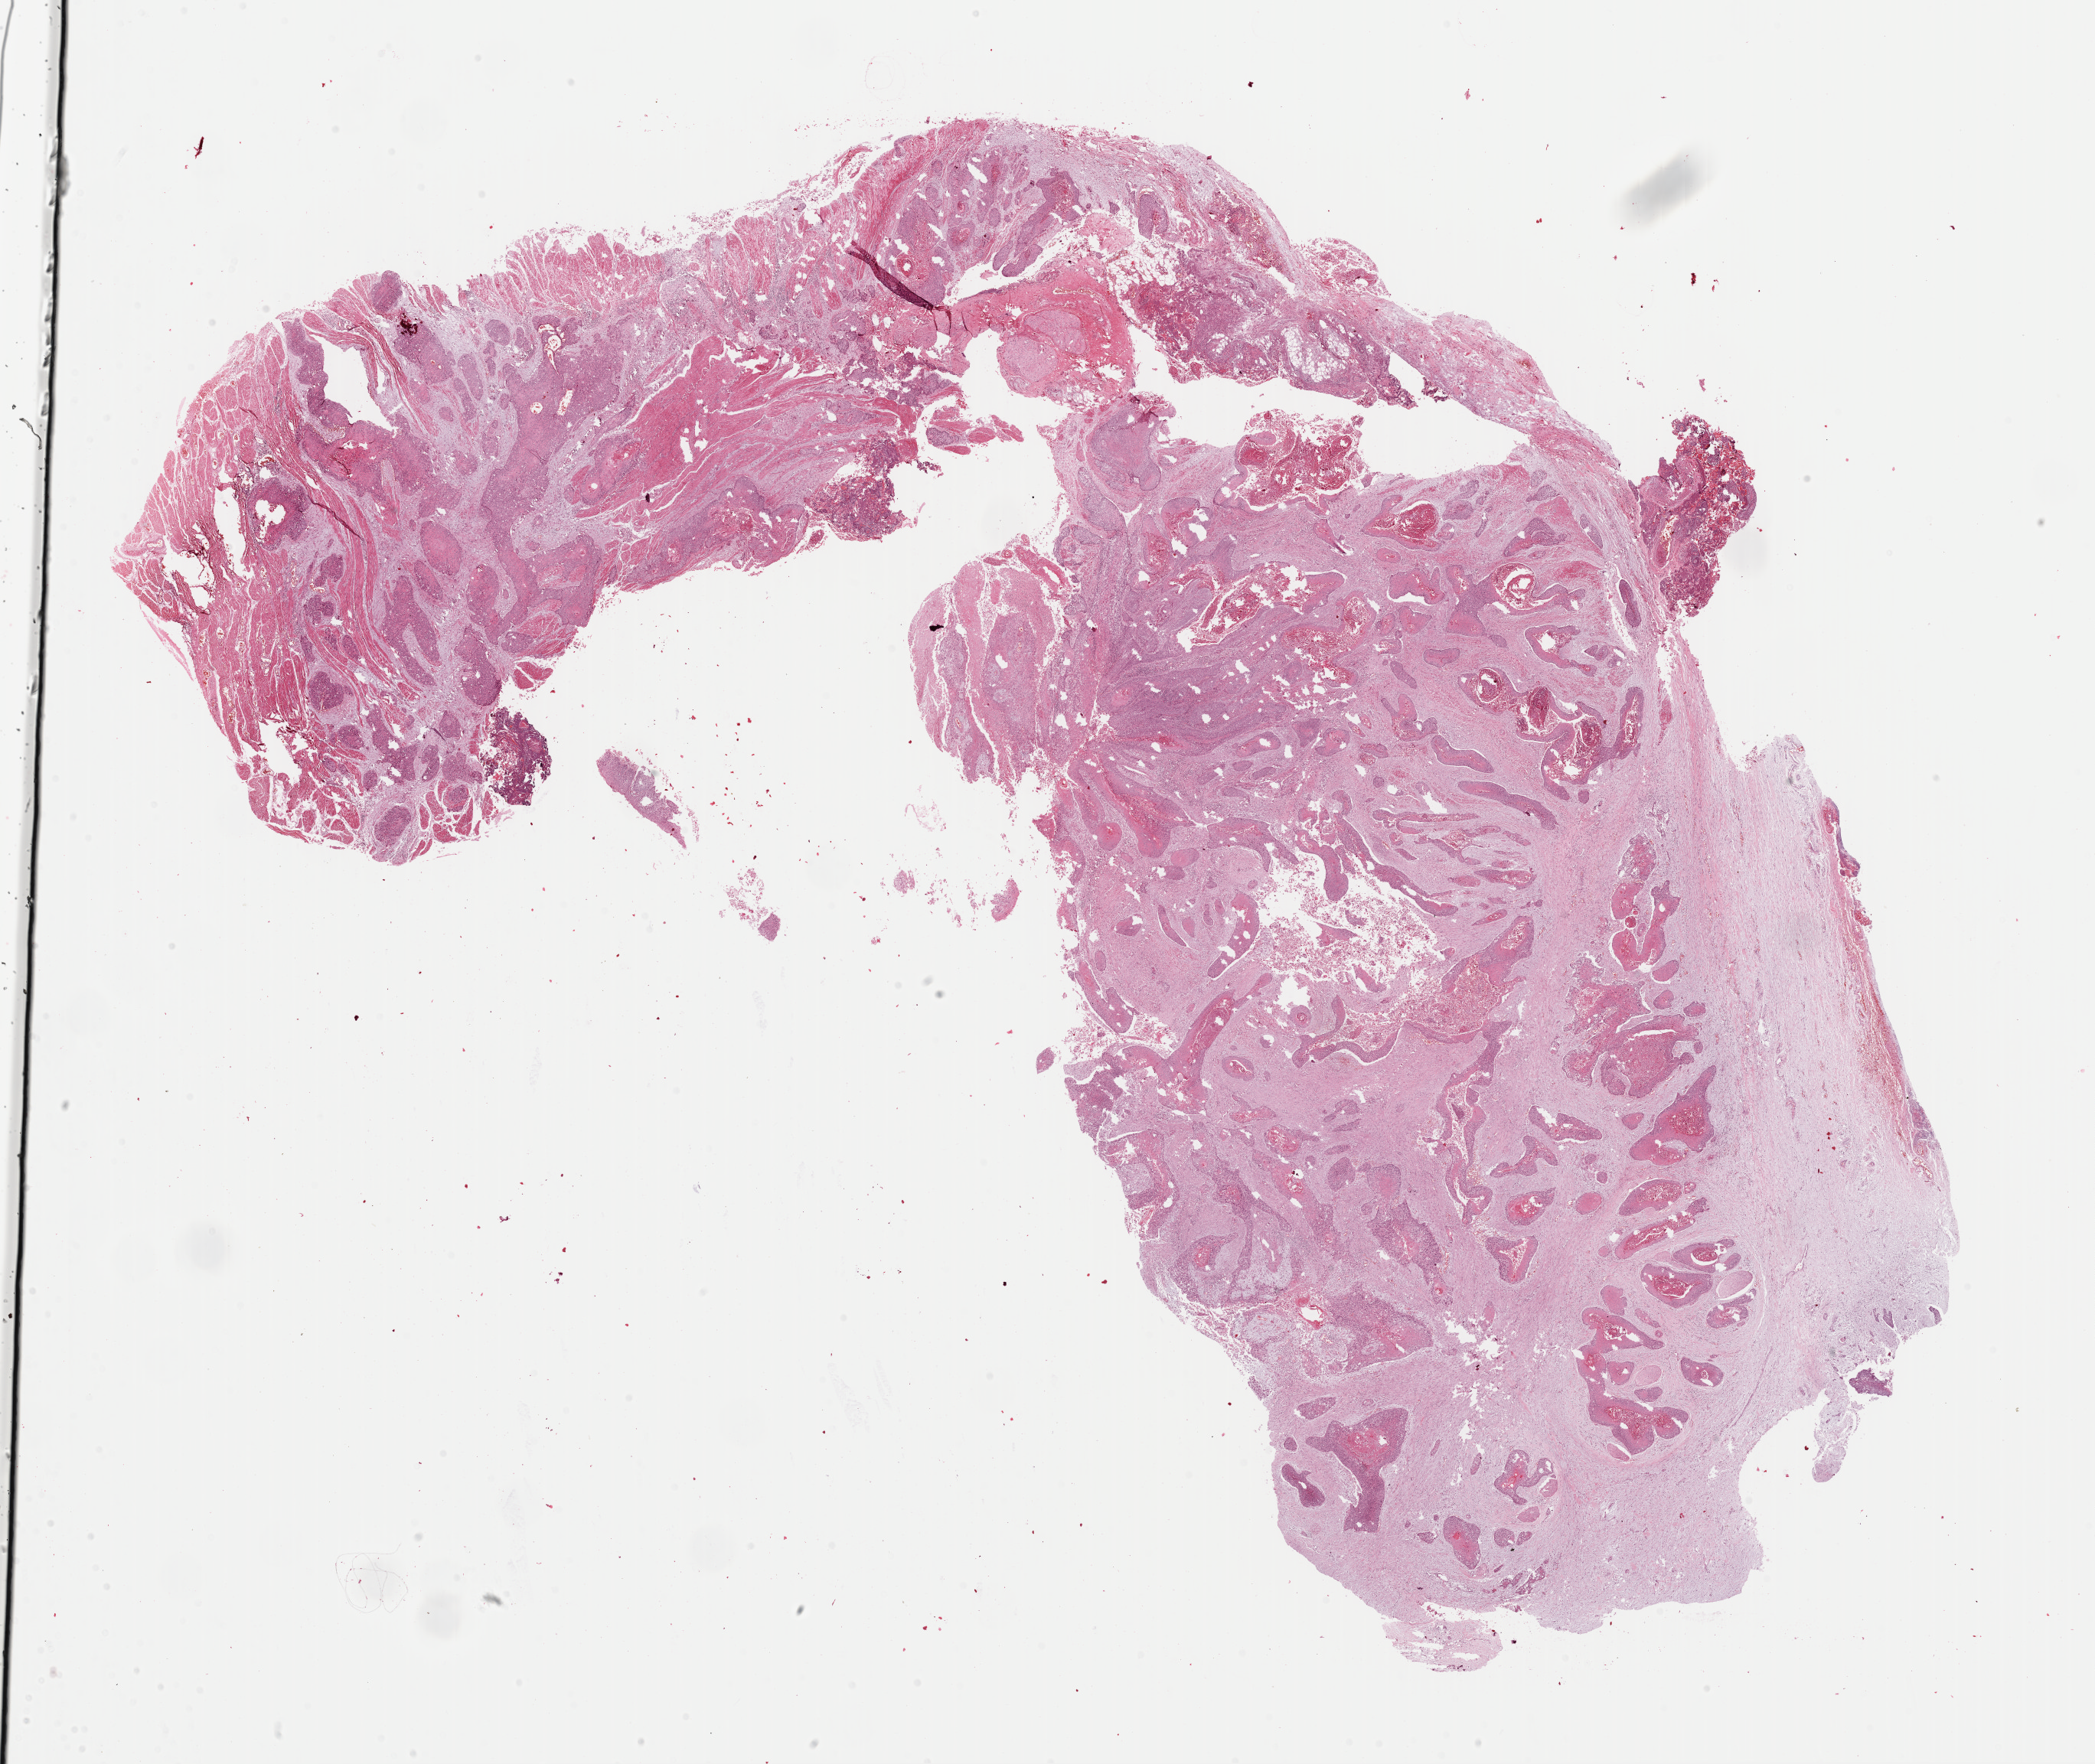
Whole-slide histology image, H&E-stained — shown as a low-resolution overview of the whole scanned area (about 21.6 x 18.2 mm). Formalin-fixed paraffin-embedded (FFPE) diagnostic section. Esophagus, primary tumour sample. Male, age 36 years at initial diagnosis. Histologic grade: GX (grade cannot be assessed).
Histologic diagnosis: Squamous cell carcinoma, NOS. TNM: T3 N1 M0. AJCC pathologic stage: III (6th edition).